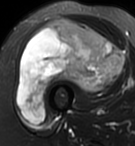
MRI of an extremity soft-tissue mass, one axial slice; T2-weighted fat-saturated; MR volume resampled by the dataset authors to the PET/CT grid (not the native acquisition matrix); 3.27 mm slice thickness; 135 × 146 image matrix, field of view 132 × 143 mm. Female patient. Case-level facts recorded for this patient, not image findings: histological type: pleiomorphic undifferentiated sarcoma; grade: high; site of the primary tumour: right quadricep.
Outlined on this slice (expert contour drawn on MRI and transferred to this co-registered scan by the dataset authors):
- gross tumour volume including surrounding oedema: bounding box <18,18,125,124> (left, top, right, bottom; pixels)
- gross tumour volume (mass): <18,18,125,124>